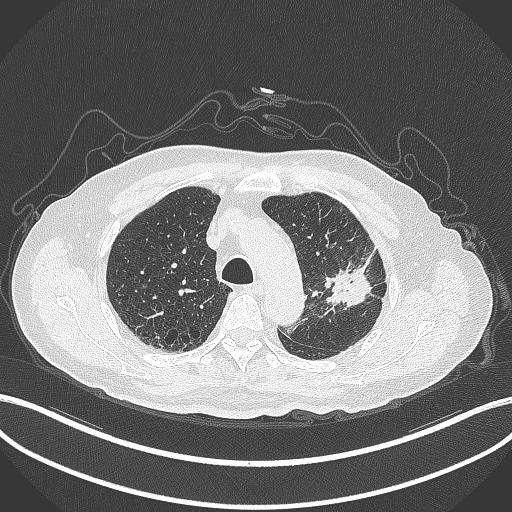
Chest CT, one axial slice; slice 222 of 331 in the series (ordered by position); reconstruction kernel B70f; lung window (W 1500 / L -600 HU); 1 mm slice thickness; 512 × 512 image matrix. Patient: male, 79 years. From the clinical record (not read from this slice): clinical TNM (as recorded): T2a N1 M1; histopathological grade: G3.
Structures marked on this image (rectangle marked by the reading radiologist):
- lung tumour (recorded histology: adenocarcinoma): box from (x=320, y=250) to (x=382, y=311) px